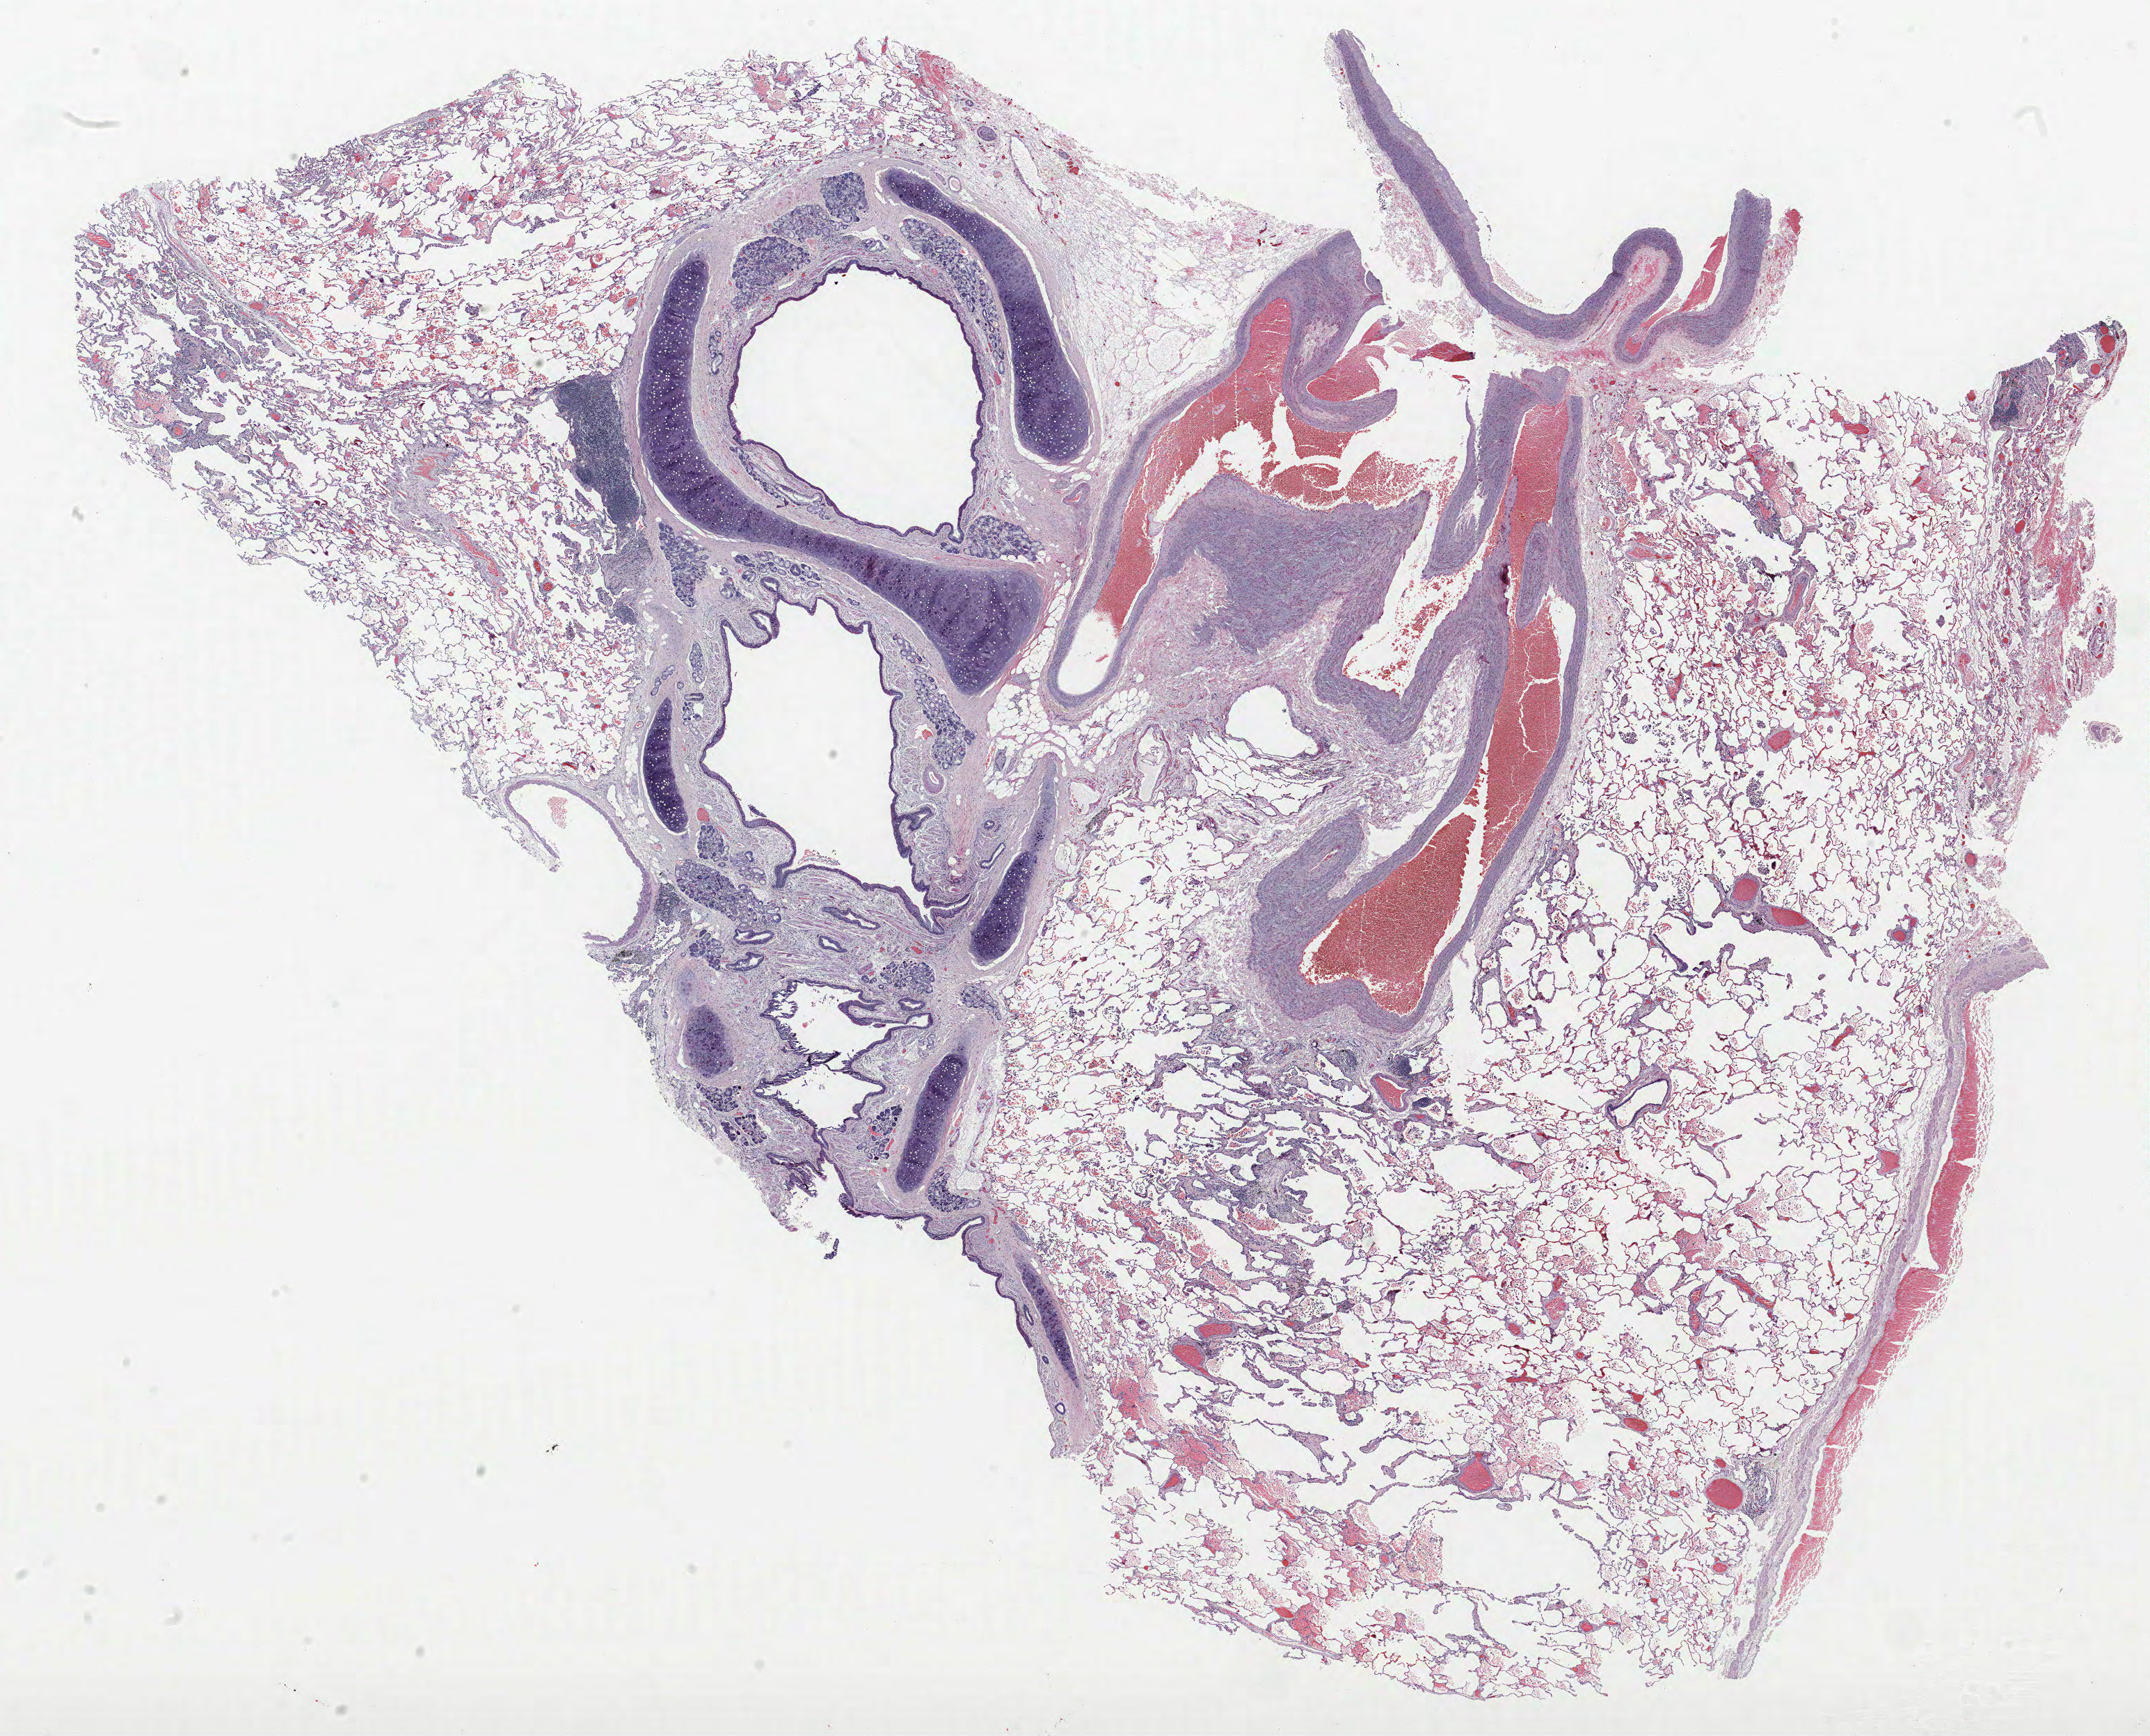
Hematoxylin and eosin (H&E) stained whole-slide image, a low-resolution overview of the entire scanned area, about 24.7 x 20.0 mm. Formalin-fixed paraffin-embedded (FFPE) section. Lung. Female, age 62 at enrolment. Grade: poorly differentiated (G3).
Stage (AJCC 6th edition): IB. Tumour size (pathology): 12 mm. Participant's lung-cancer diagnosis: Adenocarcinoma, NOS. Primary tumour location (clinical record): right upper lobe.